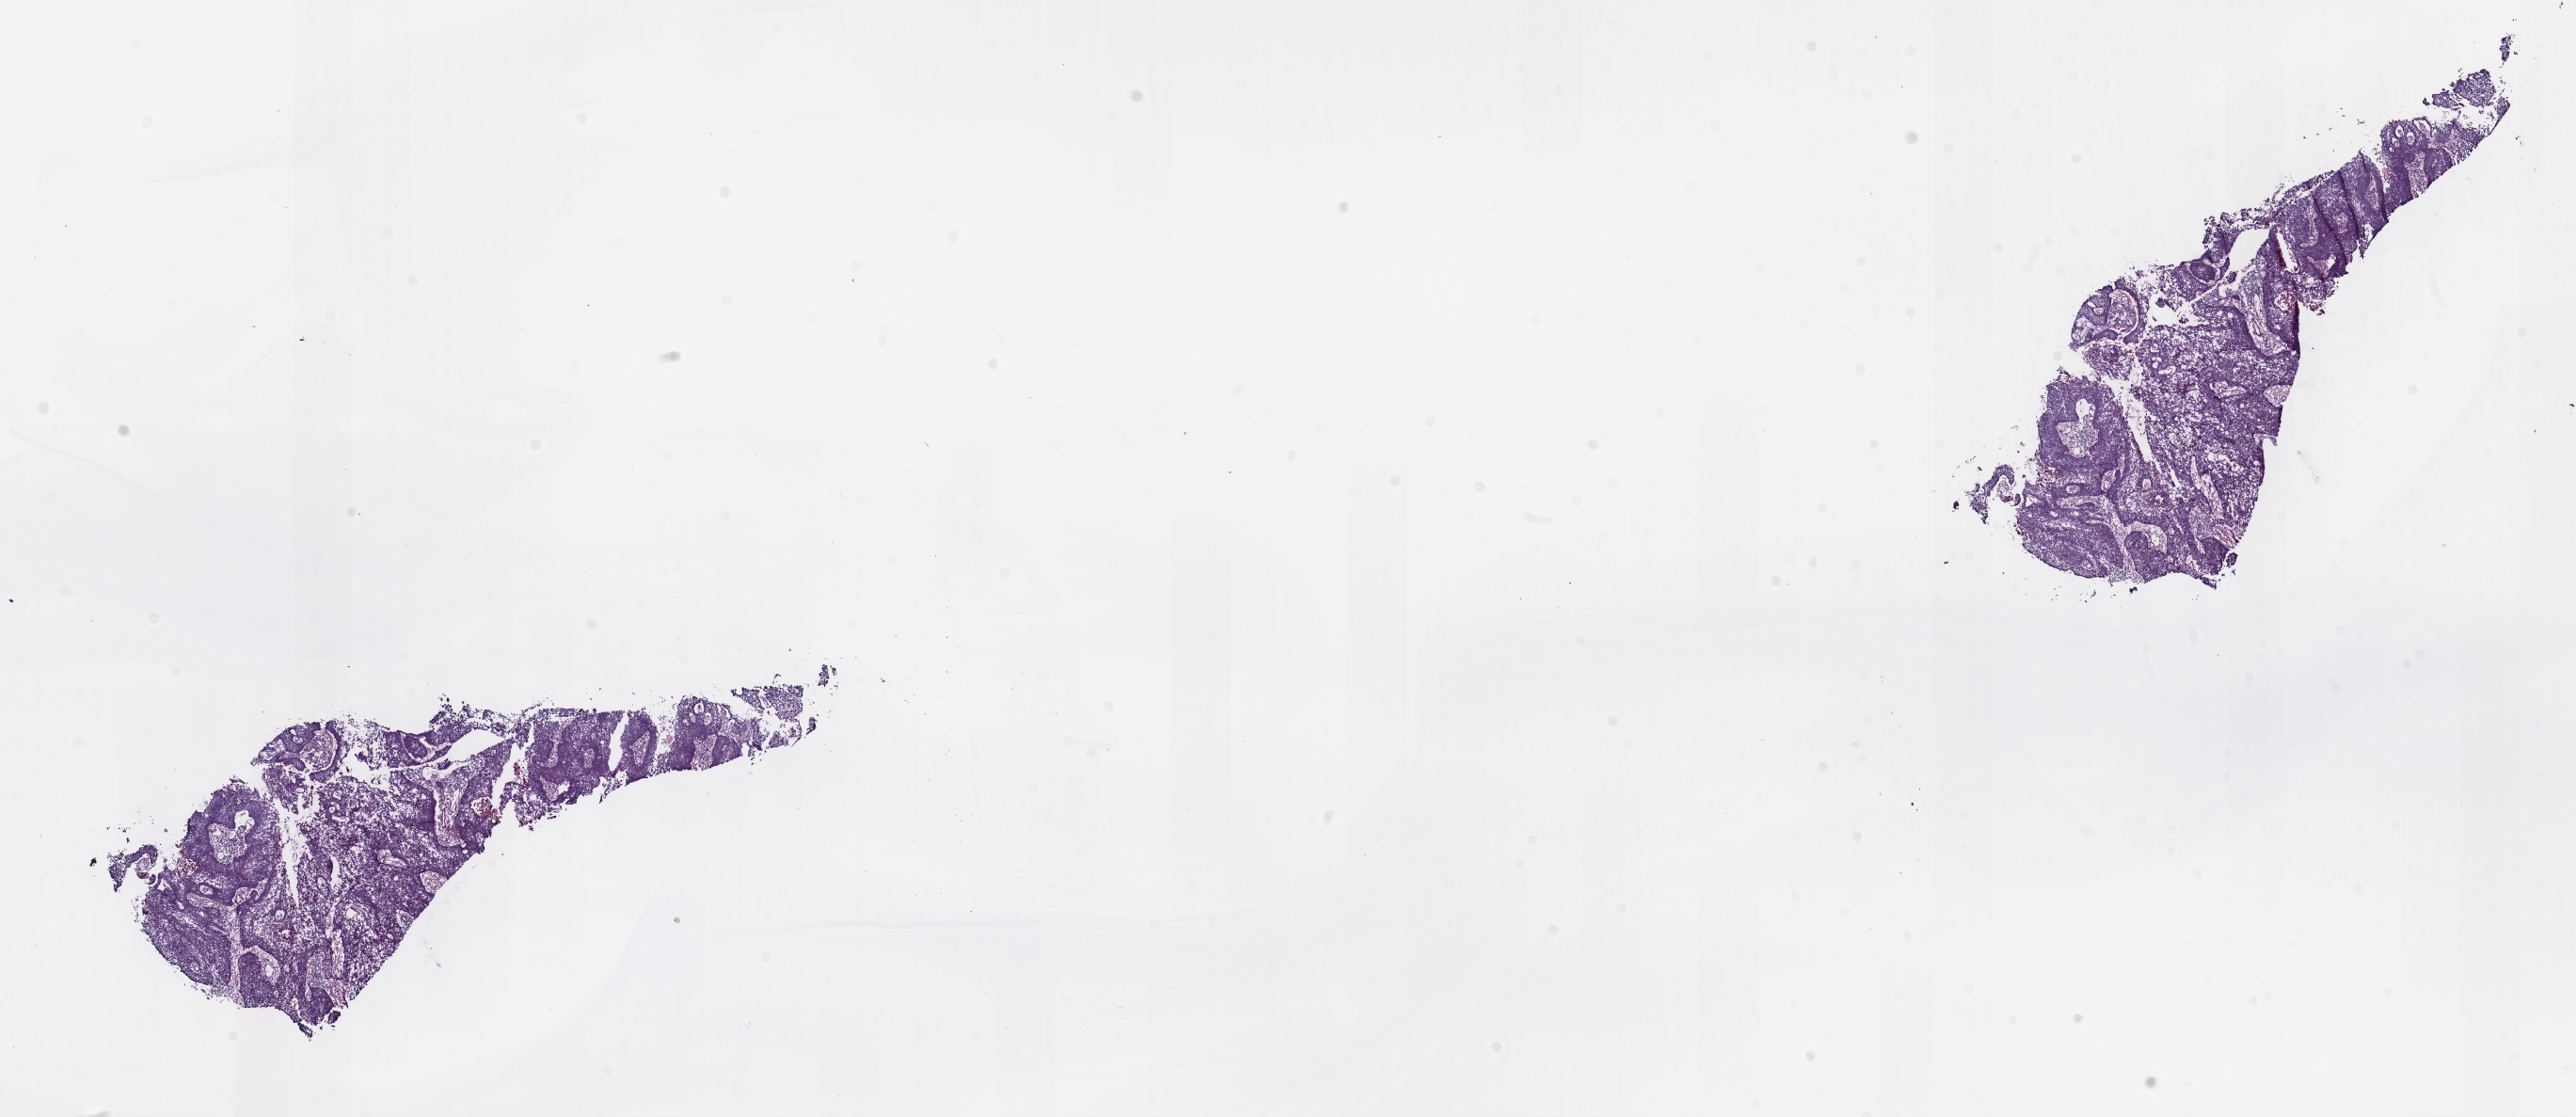
Whole-slide histology image, H&E — whole scanned area (about 22.1 x 9.6 mm, slide scanned at 40x) shown as a low-resolution overview. Frozen section from the top of the tissue portion. Cervix, primary tumour sample. Patient: female, age at initial diagnosis 37 years. Histologic grade: G2 (moderately differentiated). Composition of this section per pathologist review: tumour cells 75%, tumour nuclei 75%, normal cells 5%, stromal cells 15%, necrosis 5%. Infiltration values recorded for this section: lymphocyte infiltration 4%, monocyte infiltration 0%, neutrophil infiltration 1%.
Lymph nodes positive (case pathology): 0 of 33 examined. Histologic diagnosis: Squamous cell carcinoma, NOS (cervix uteri). FIGO stage: IB.